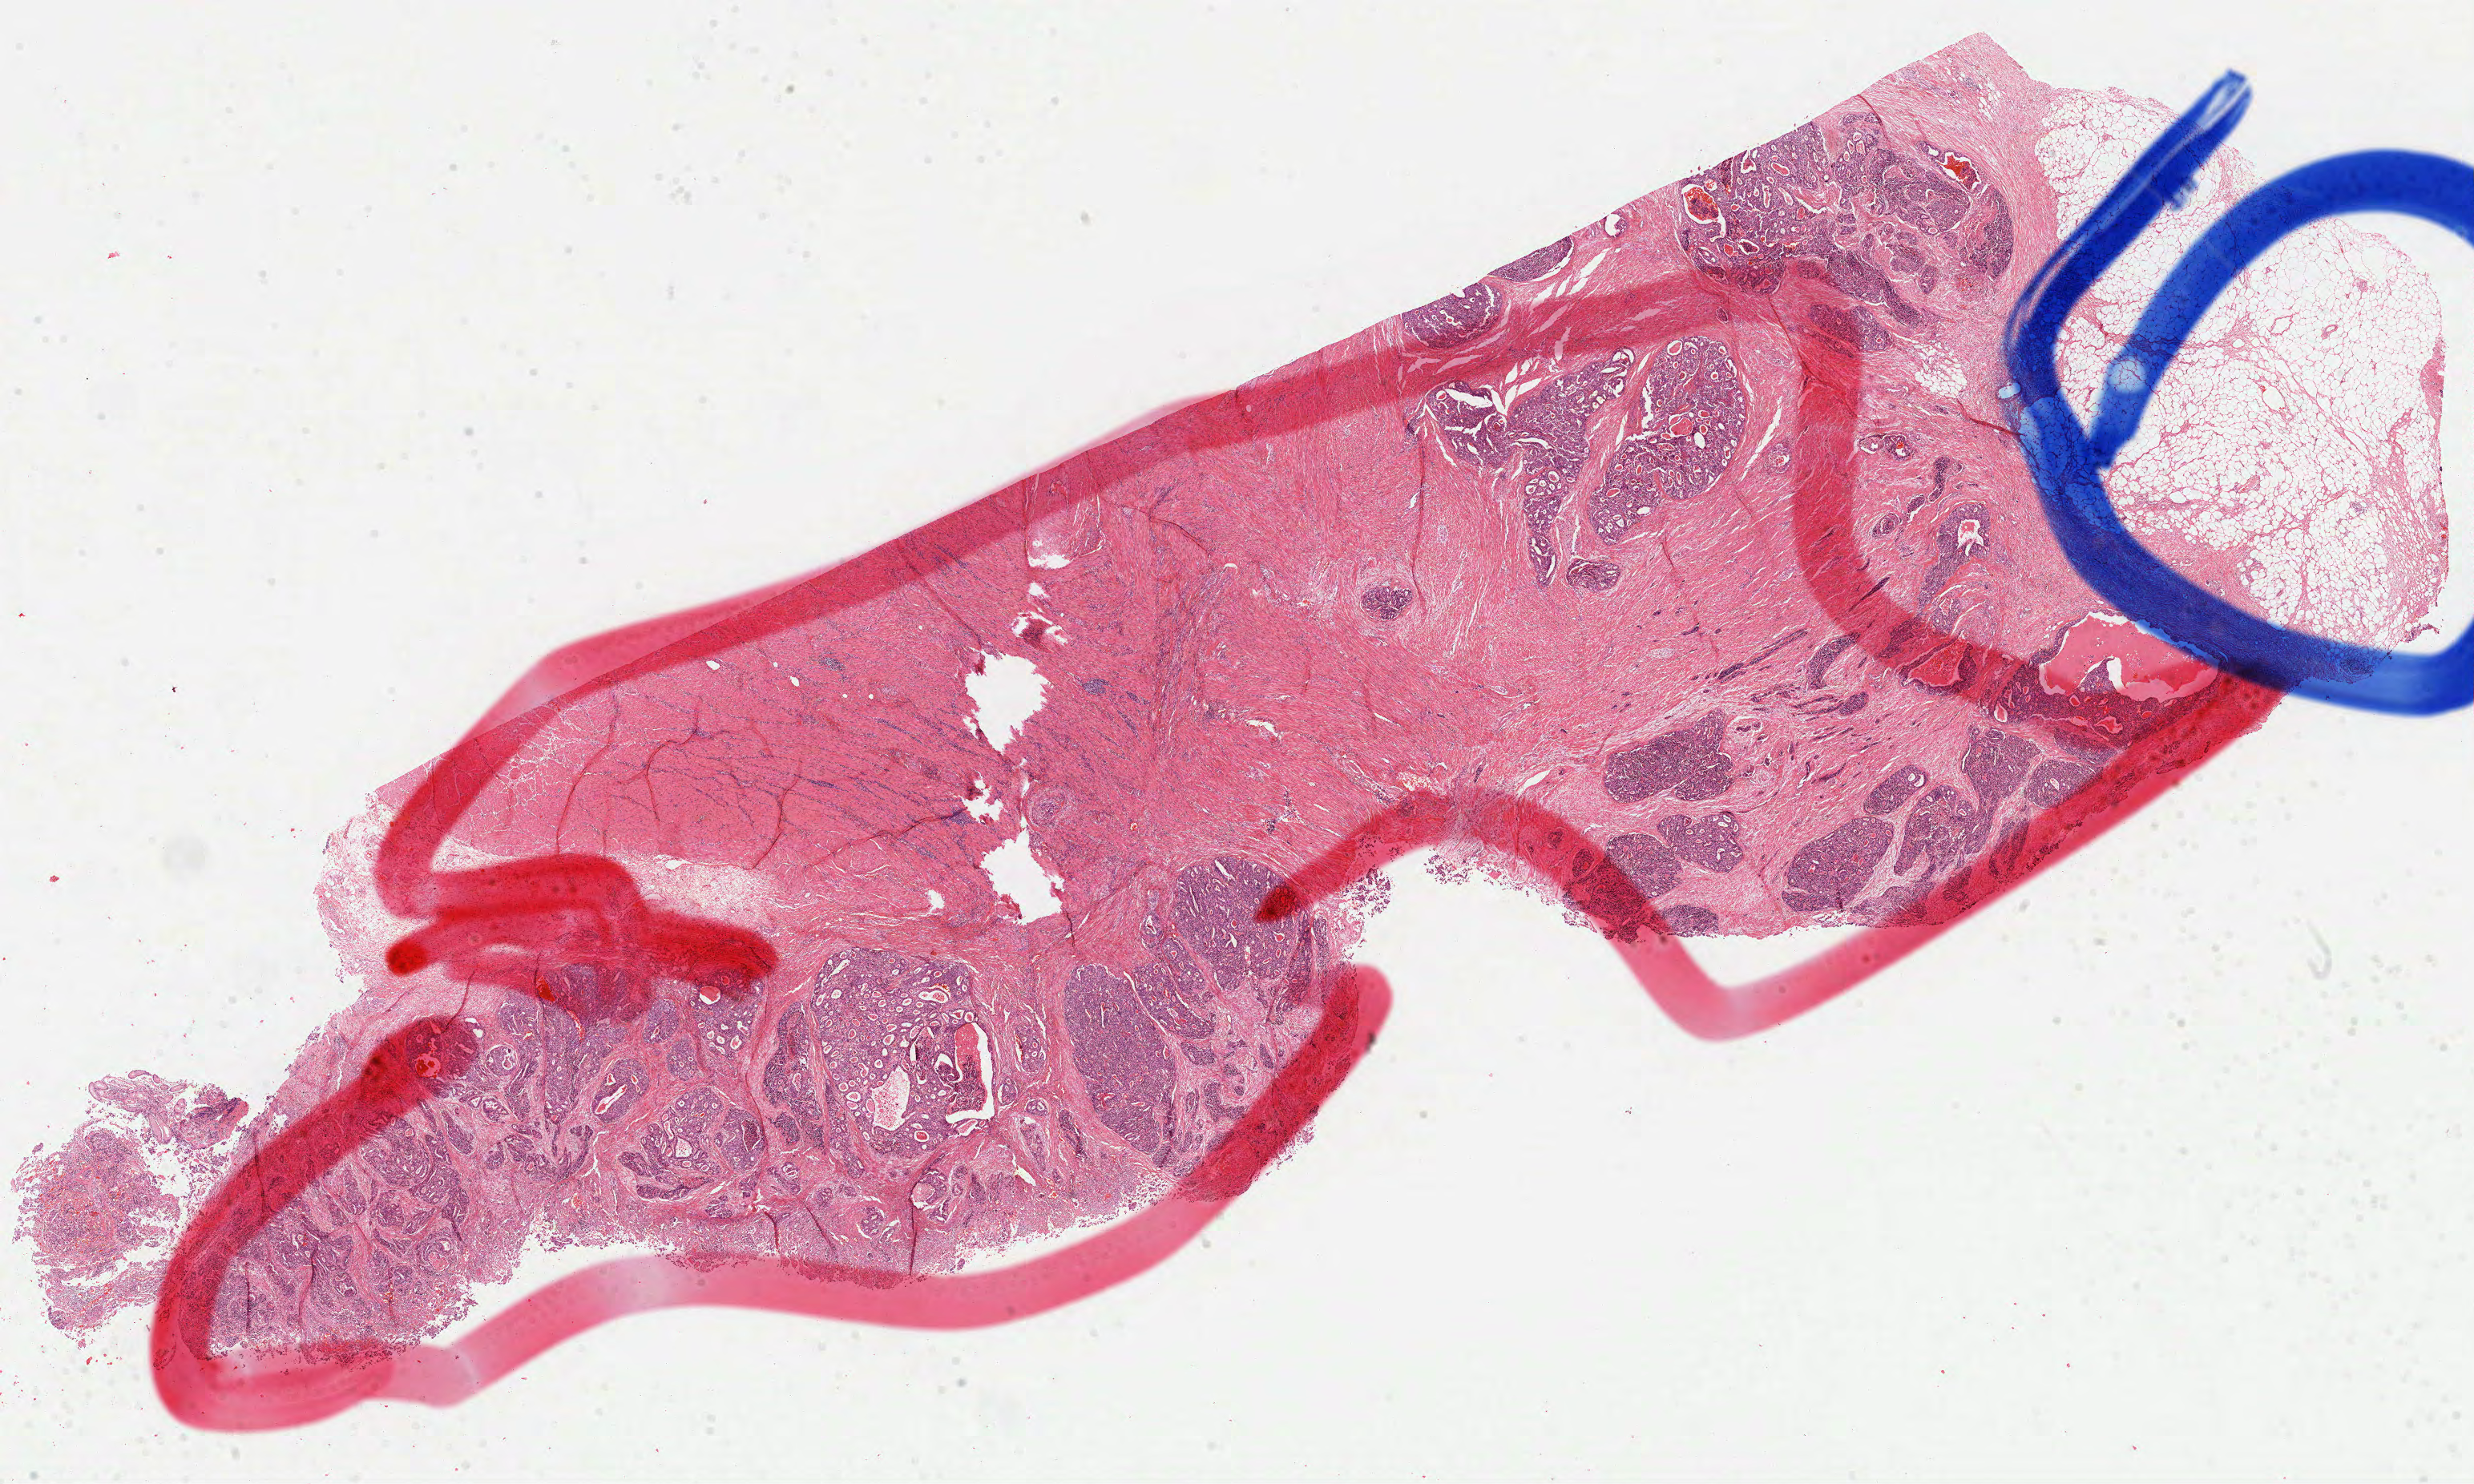
H&E-stained whole-slide image — whole scanned area (about 24.9 x 14.9 mm, slide scanned at 40x) shown as a low-resolution overview, formalin-fixed paraffin-embedded (FFPE) diagnostic section, sample: primary tumour, stomach. Male patient; age at initial diagnosis 69 years. Histologic grade: GX (grade cannot be assessed).
Lymph nodes positive (case pathology): 0 of 15 examined. AJCC pathologic stage: II (7th edition). Pathologic diagnosis: Adenocarcinoma, NOS (gastric antrum). TNM: T3 N0 M0.